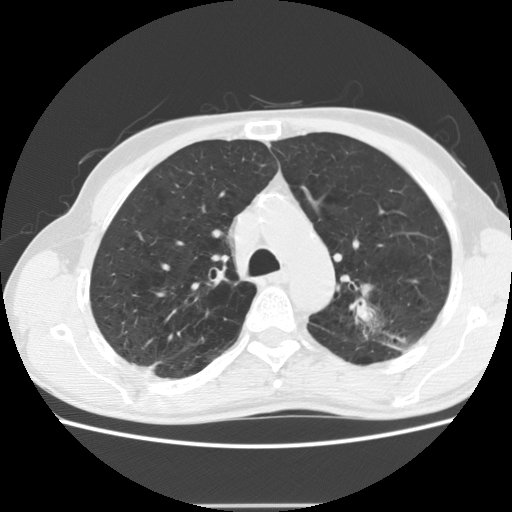
Axial slice from a low-dose chest CT screening exam; baseline screening round; lung window (W 1500 / L -600 HU); slice 53 of 191 in the series. Male participant, aged 64 years at enrolment. Current smoker at enrolment.
Expert-annotated lung lesion, box from (x=338, y=279) to (x=442, y=360) px. Screening reader's record for this exam (one nodule recorded; not confirmed to be the boxed lesion): non-calcified nodule or mass ≥4 mm, left upper lobe, 27 × 19 mm, poorly defined margins, soft tissue attenuation. Later outcome: lung cancer diagnosed 23 days after this screen — adenocarcinoma, NOS, left upper lobe, moderately differentiated (G2), stage IA (AJCC 6th edition), 29 mm at pathology.